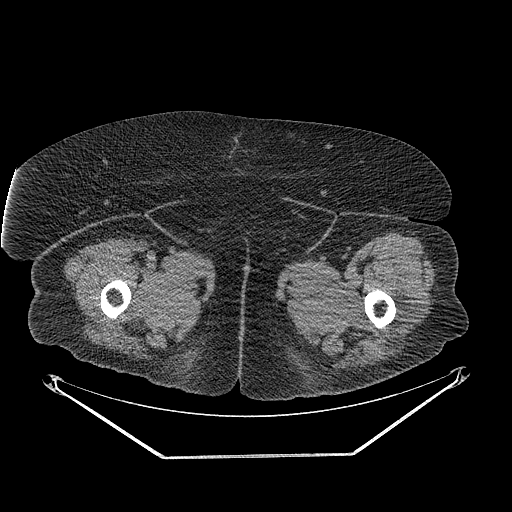
CT of an extremity soft-tissue mass (from a PET/CT study), one axial slice; slice 261 of 267 in the series (ordered by position); reconstruction kernel STANDARD; soft-tissue window (W 400 / L 40 HU); 512 × 512 image matrix, field of view 500 × 500 mm. Female patient. Case-level facts recorded for this patient, not image findings: histological type: undifferentiated – high grade; grade: high; site of the primary tumour: left thigh.
Annotated regions visible in this slice (expert contour drawn on MRI and transferred to this co-registered scan by the dataset authors):
- gross tumour volume including surrounding oedema: box from (x=399, y=301) to (x=412, y=314) px